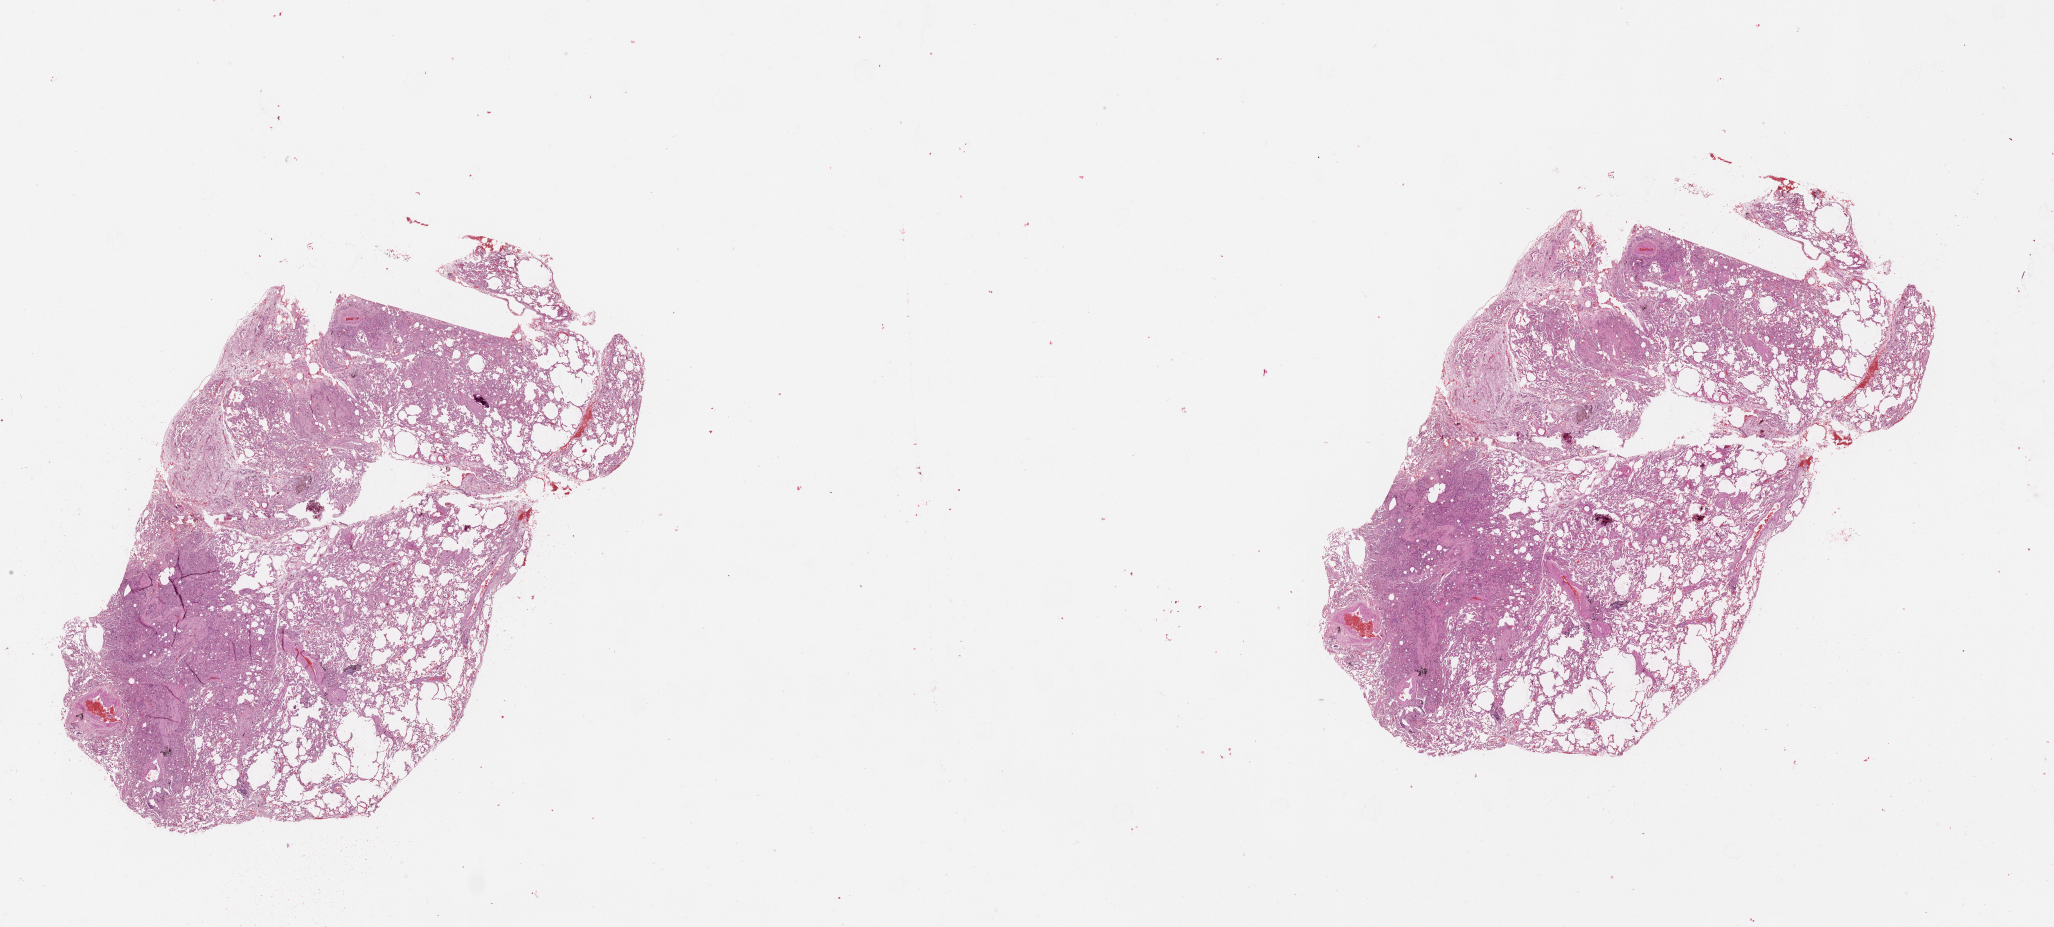
Whole-slide histology image, H&E — a low-resolution overview of the entire scanned area, about 33.1 x 14.9 mm. Normal (non-tumour) tissue sample, lung. Male, 59 y/o.
• this section: normal (non-tumour) tissue from the same patient
• patient diagnosis (cohort enrolment): squamous cell carcinoma (lung)